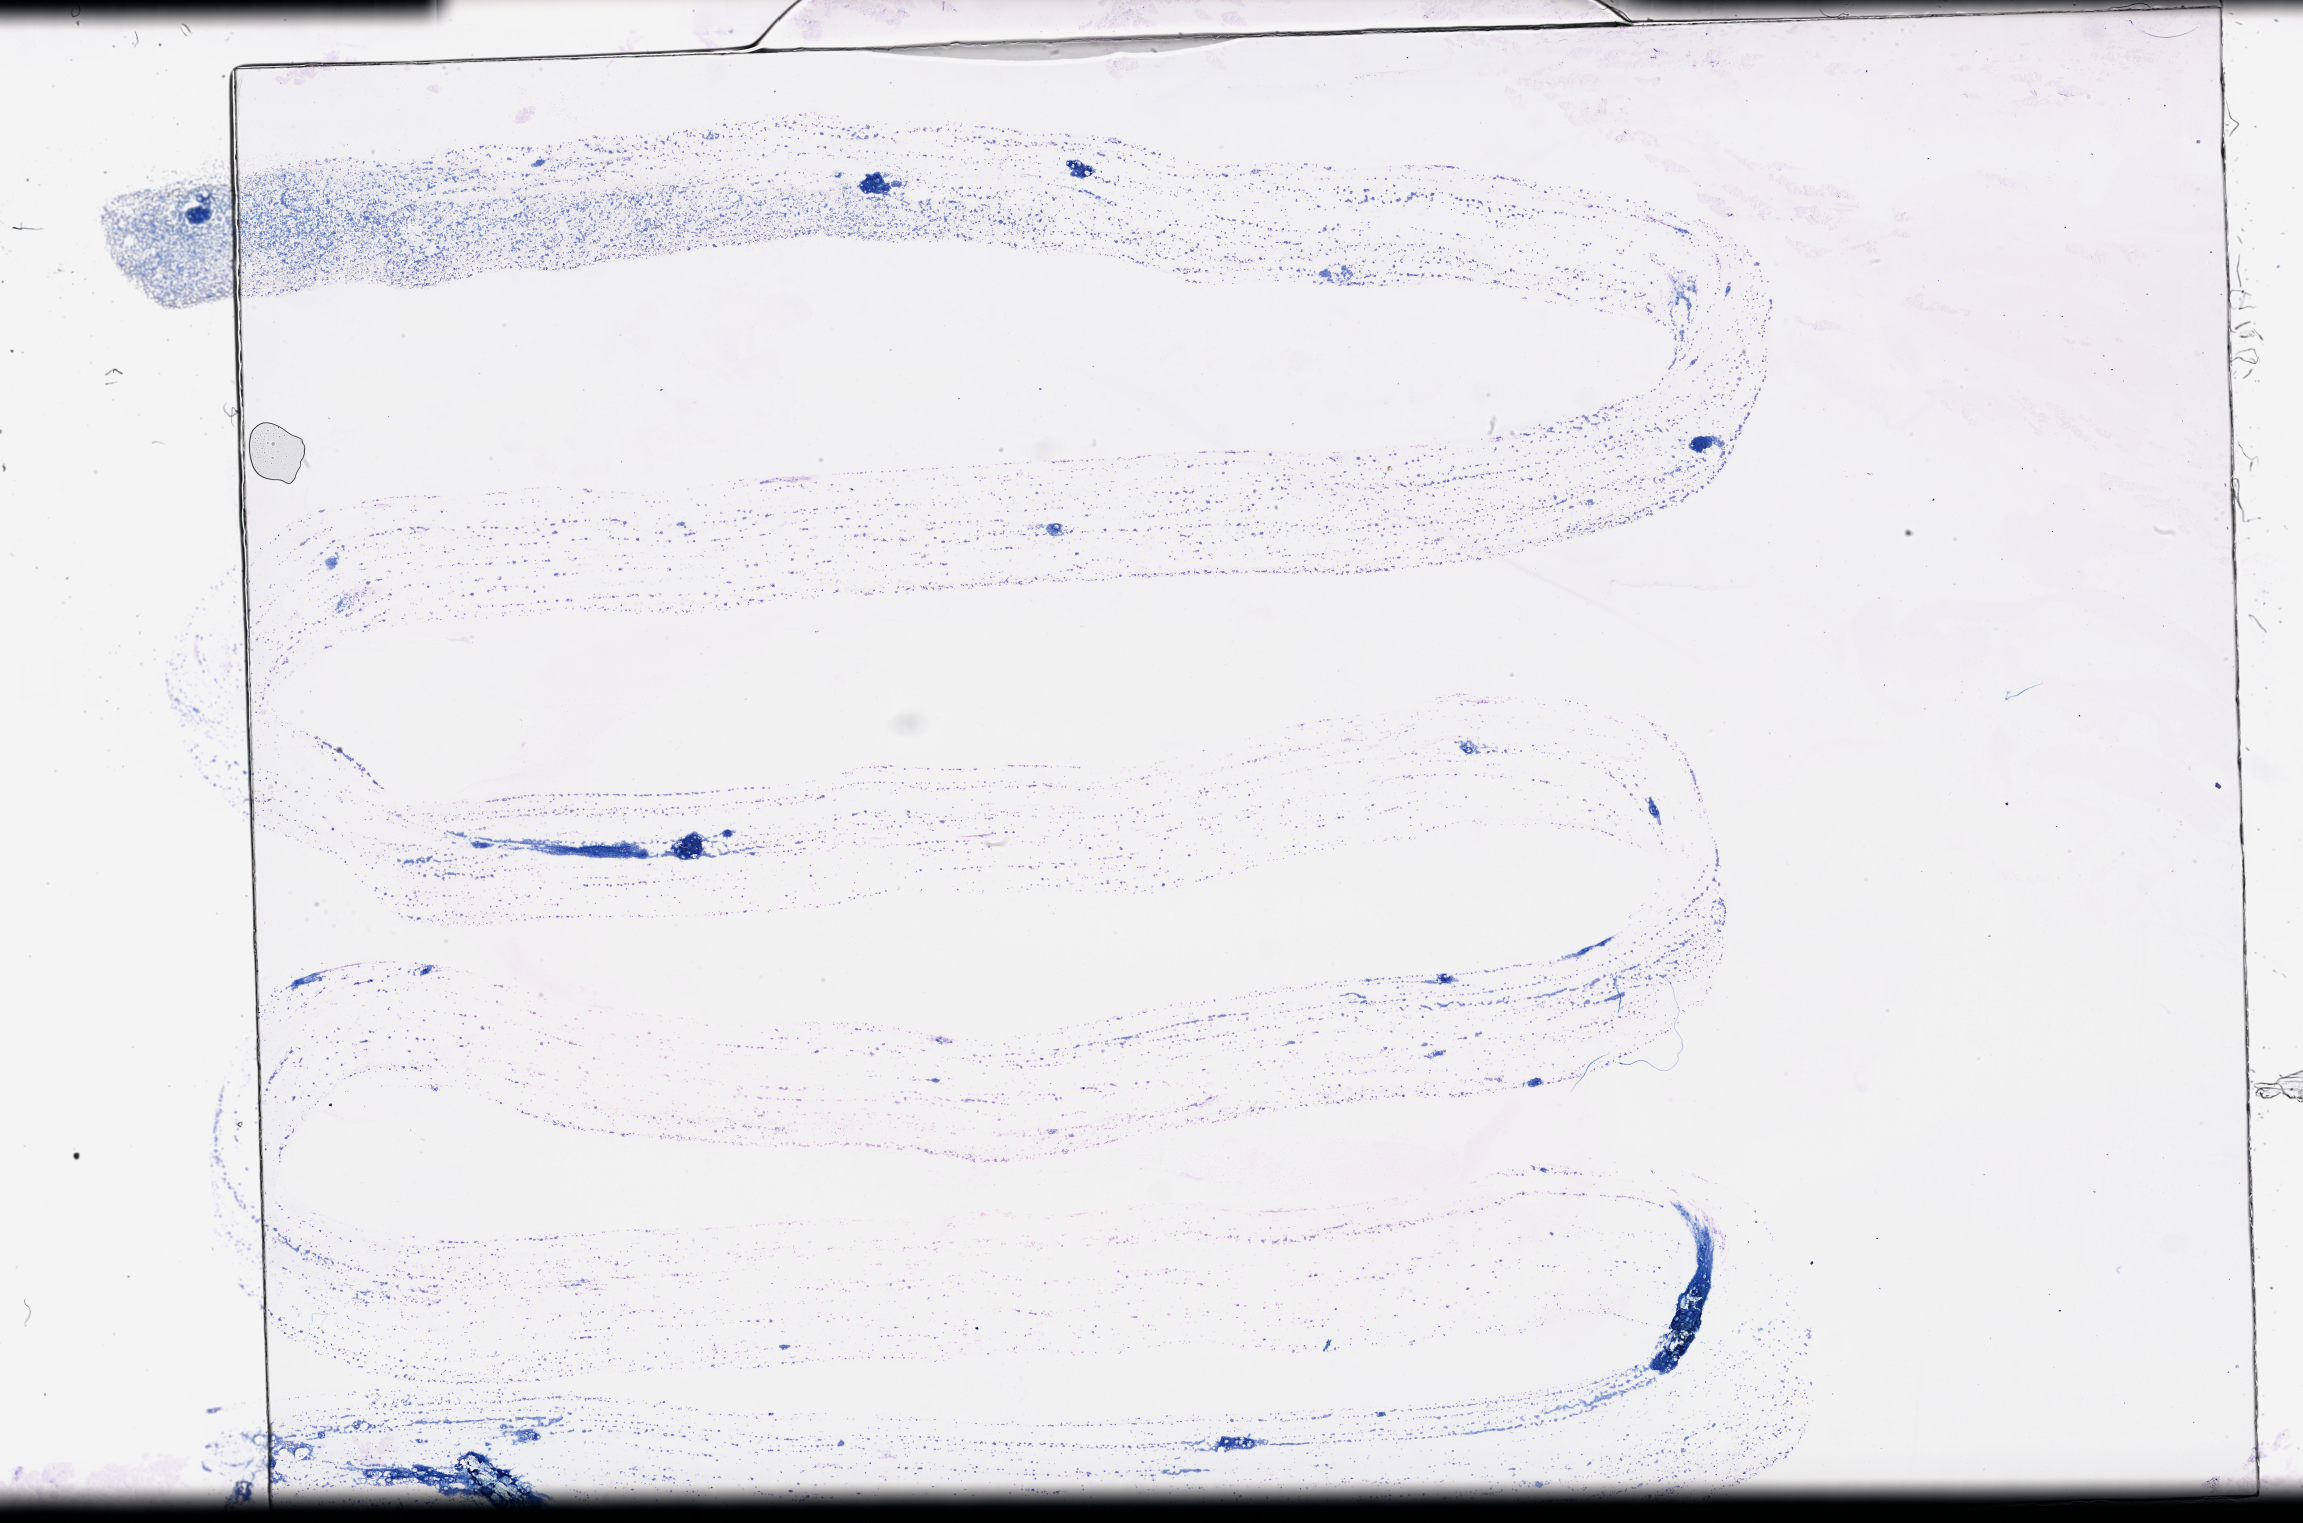
Digitized Hematoxylin and eosin (H&E) stained tissue section (whole slide), shown as a low-resolution overview of the whole scanned area (about 37.2 x 24.6 mm); bone marrow (leukaemic) sample. Patient: female, age 75 years. Blasts: 50%.
Diagnosis: Acute Myeloid Leukemia. WHO classification: AML with myelodysplasia-related changes. FAB classification: M4.